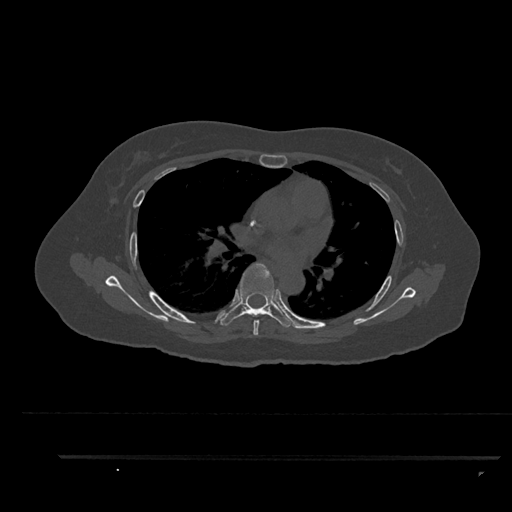
CT including the spine, one axial slice. Position 571 of 797 along the scan axis. Reconstruction kernel Br40s/3. Bone window (W 1800 / L 400 HU). 0.5 mm slice thickness. 512 × 512 image matrix, field of view 408 × 408 mm. Female patient, age 44 years. From the clinical record (not read from this slice): primary cancer: renal.
Structures marked on this image (semi-automatically segmented with operator editing):
- T5 vertebra: bounding box <253,320,260,335> (left, top, right, bottom; pixels)
- T6 vertebra: <220,263,295,328>